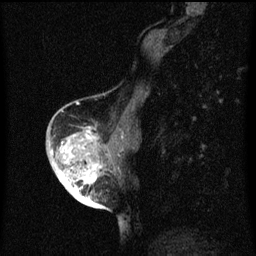
Breast MRI (dynamic contrast-enhanced), one sagittal slice; slice 25 of 60 in the series (ordered by position); dynamic contrast-enhanced series, image 2 of 3 at this slice position (ordered by acquisition); 1.5 T; TE 4.2 ms, TR 8 ms; 2 mm slice thickness; 256 × 256 image matrix. Female patient, age 56 years.
Structures marked on this image (semi-automatic segmentation, software-assisted and operator-edited):
- analysis volume of interest (the breast-tissue region the enhancement analysis was run in; not a lesion): box from (x=54, y=128) to (x=118, y=199) px
- tumour enhancement mask (voxels above the 70 % enhancement threshold inside the analysis volume of interest): (x=56, y=128)–(x=101, y=199)